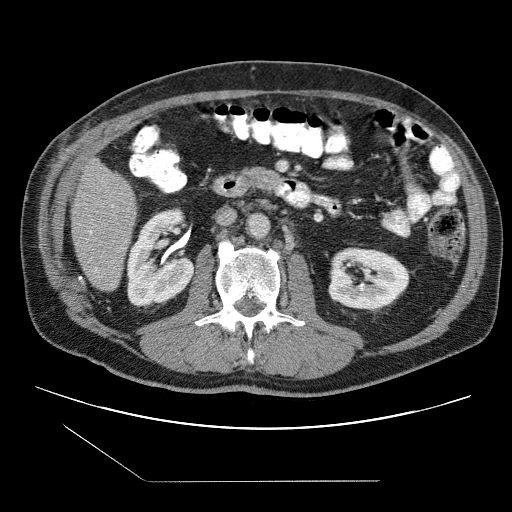
Contrast-enhanced abdominal CT (liver protocol), one axial slice. Slice 25 of 109 in the series (ordered by position). One of 2 acquisitions stored at this slice position. Soft-tissue window (W 400 / L 40 HU). 512 × 512 image matrix. From the clinical record (not read from this slice): diagnosis: hepatocellular carcinoma (patient treated with transarterial chemoembolisation; whether this scan precedes or follows treatment is not stated here); TNM stage (as recorded): Stage-IIIB.
Structures marked on this image (semi-automatic segmentation, software-assisted and operator-edited):
- liver parenchyma outside the tumour (the mass and vessels are separate outlines, so this box may not span the whole liver): bounding box <70,158,136,290> (left, top, right, bottom; pixels)
- liver vessels: <89,231,92,234>